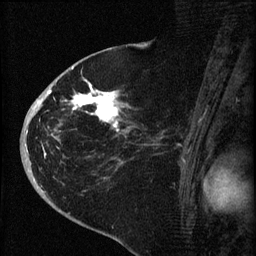
Breast MRI (dynamic contrast-enhanced), one sagittal slice; slice 38 of 60 in the series (ordered by position); dynamic contrast-enhanced series, image 2 of 4 at this slice position (ordered by acquisition); 1.5 T; TE 4.2 ms, TR 8.2 ms; 2 mm slice thickness; 256 × 256 image matrix, field of view 180 × 180 mm. Female patient, age 71 years.
Structures marked on this image (semi-automatic segmentation, software-assisted and operator-edited):
- analysis volume of interest (the breast-tissue region the enhancement analysis was run in; not a lesion): box from (x=35, y=75) to (x=150, y=190) px
- tumour enhancement mask (voxels above the 70 % enhancement threshold inside the analysis volume of interest): (x=35, y=79)–(x=124, y=155)